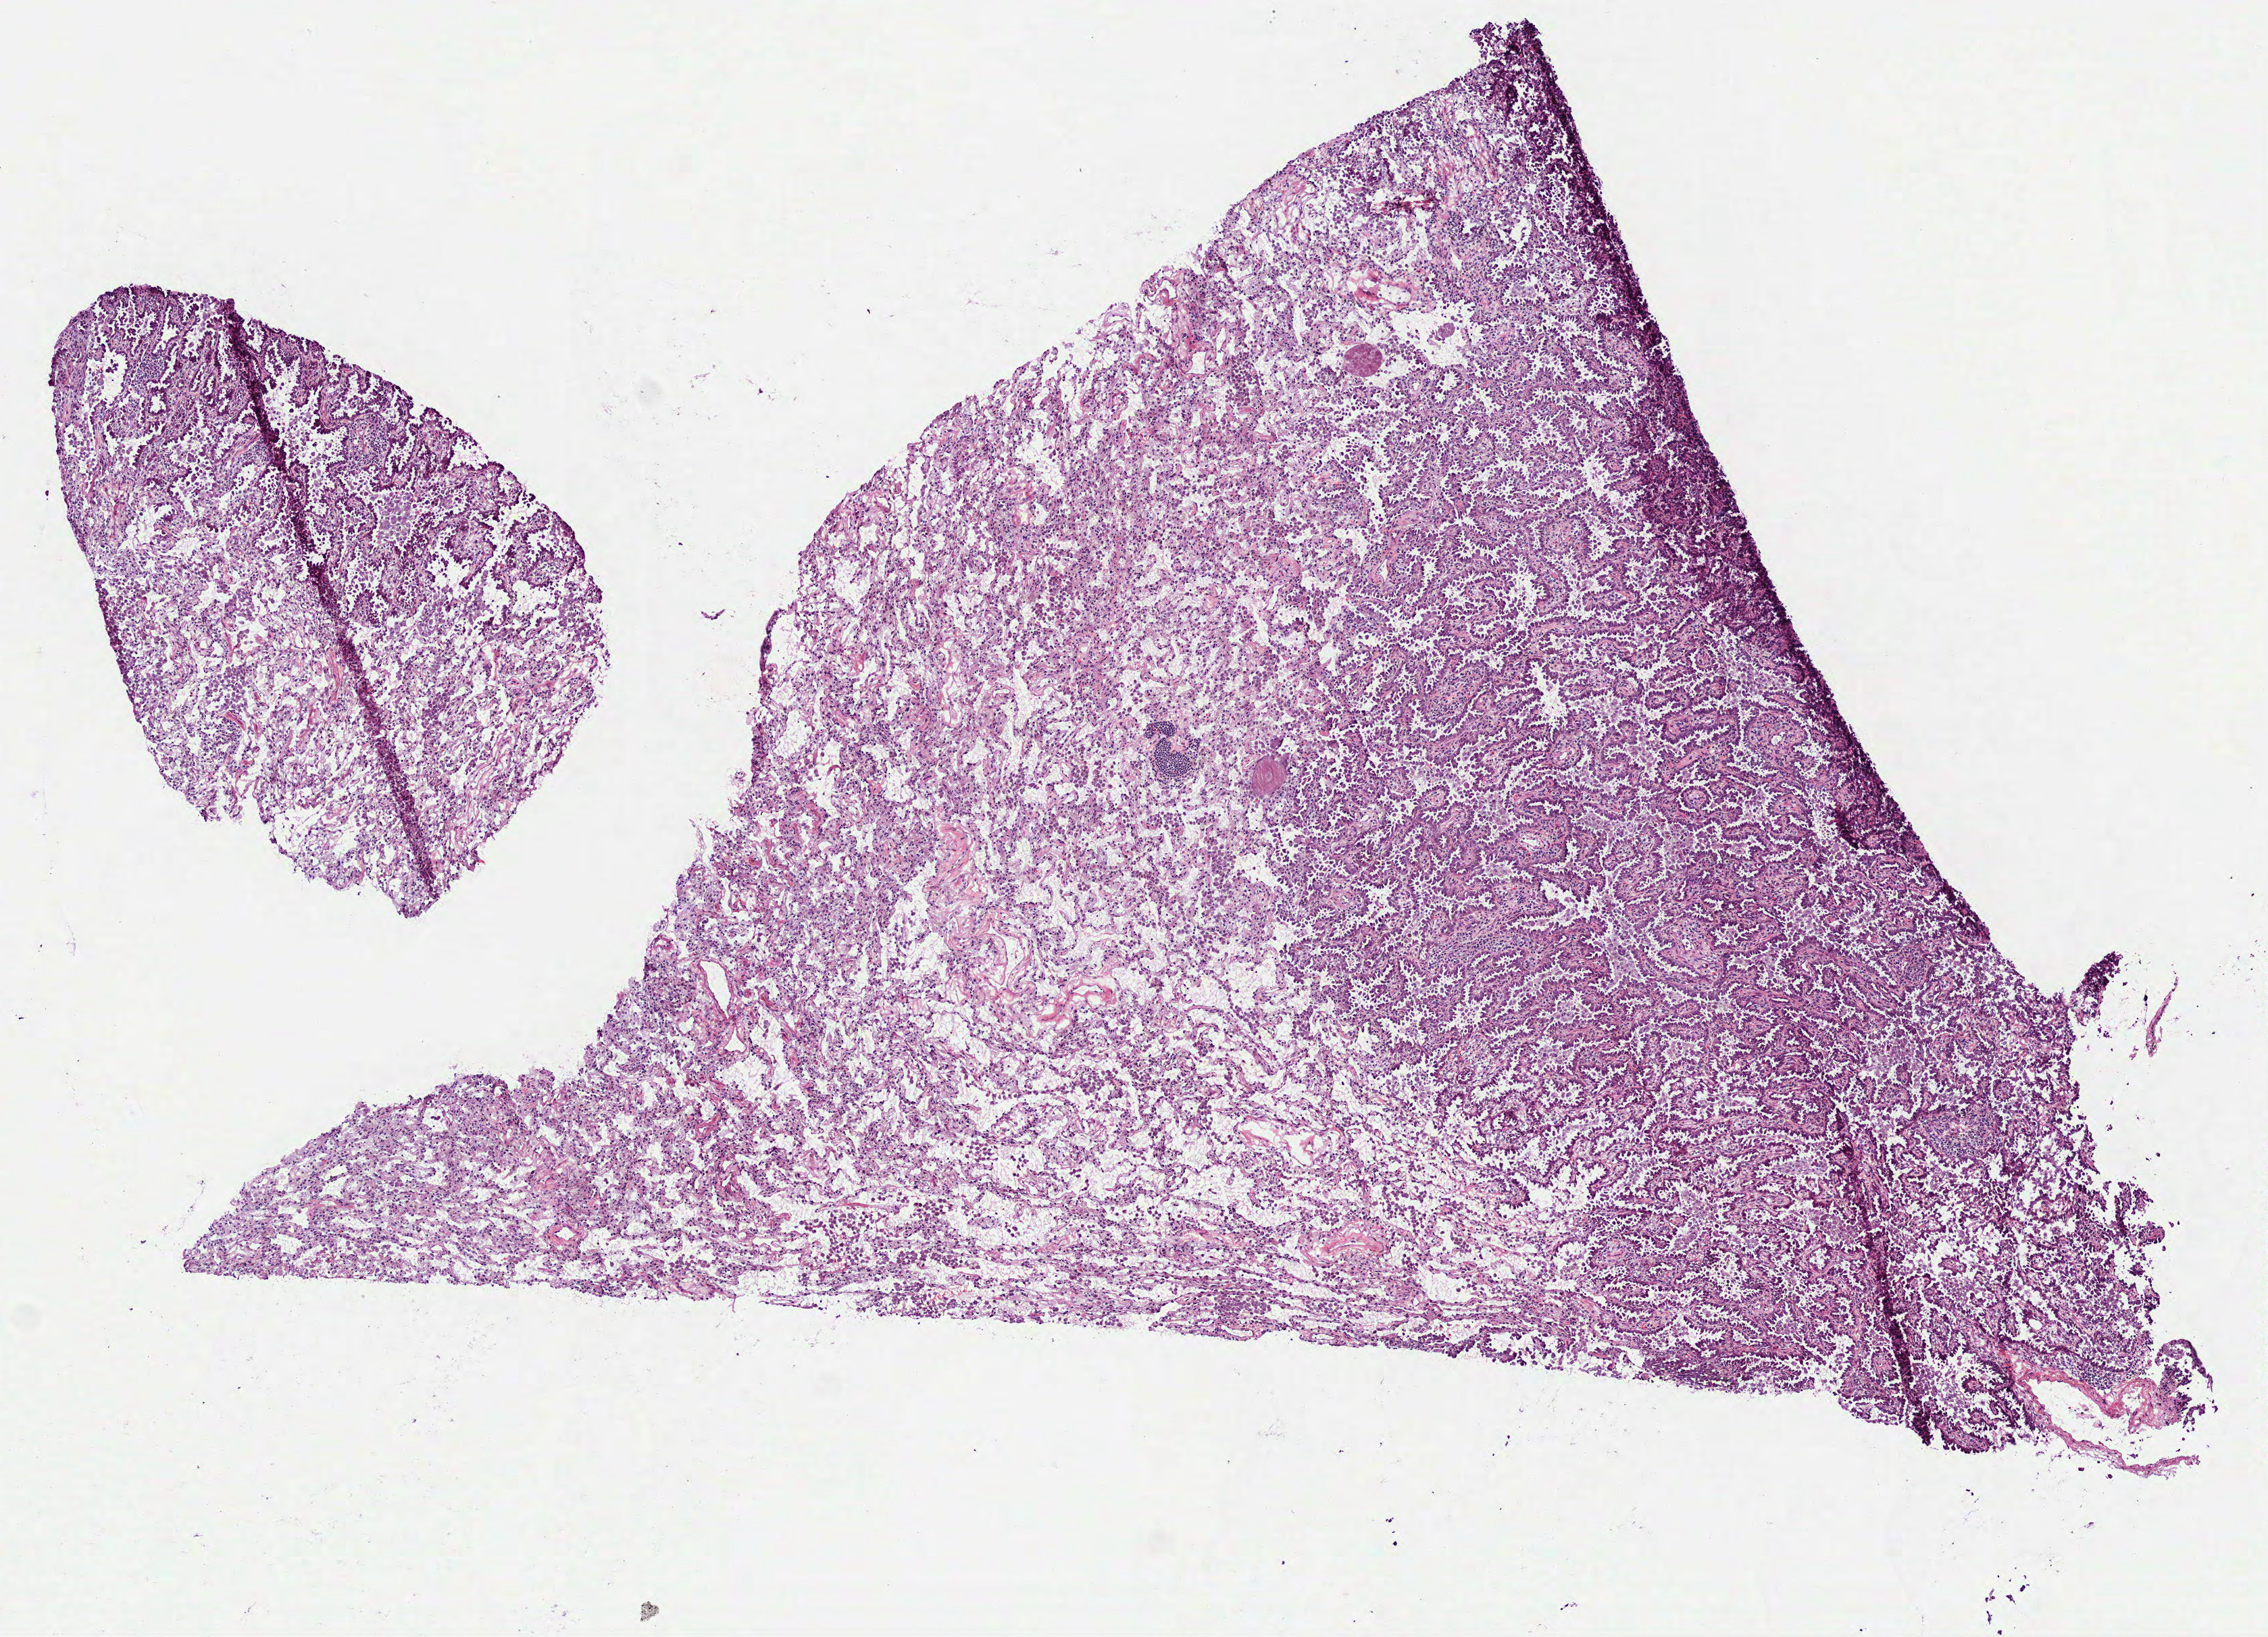
Hematoxylin and eosin (H&E) stained whole-slide image — a low-resolution overview of the entire scanned area, about 6.8 x 4.9 mm (acquisition: 40x scan); frozen section from the bottom of the tissue portion; primary tumour sample from the lung. Female patient; age at initial diagnosis 63 years. Slide review estimates, as recorded: tumour cells 30%, tumour nuclei 40%, normal cells 60%, stromal cells 10%, necrosis 0%.
AJCC pathologic stage: IB. Pathologic diagnosis: Bronchiolo-alveolar carcinoma, non-mucinous (lower lobe, lung). Laterality: left.